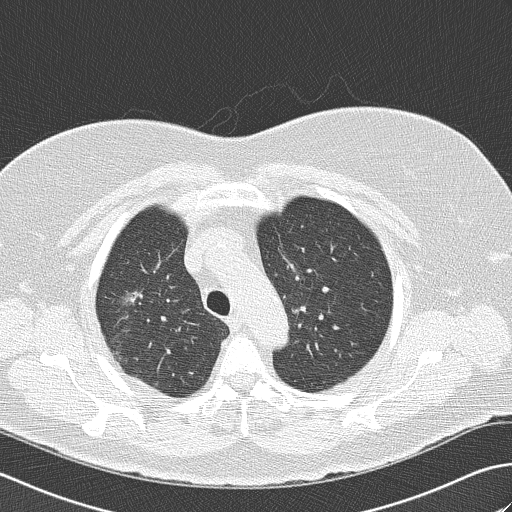
Chest CT (low-dose screening protocol), one axial image. Second screening round (one year after baseline). Lung window (W 1500 / L -600 HU). 2 mm slice thickness. Lung (sharp) reconstruction kernel (B50f). Slice 118 of 148 in the series. Female, age 74 years at enrolment. Former smoker at enrolment.
Lesion marked by an expert reader, box from (x=104, y=279) to (x=161, y=330) px. The screening reader recorded 4 non-calcified nodules or masses ≥4 mm on this exam; which of them this box marks is not recorded. Official screen result: positive, other.